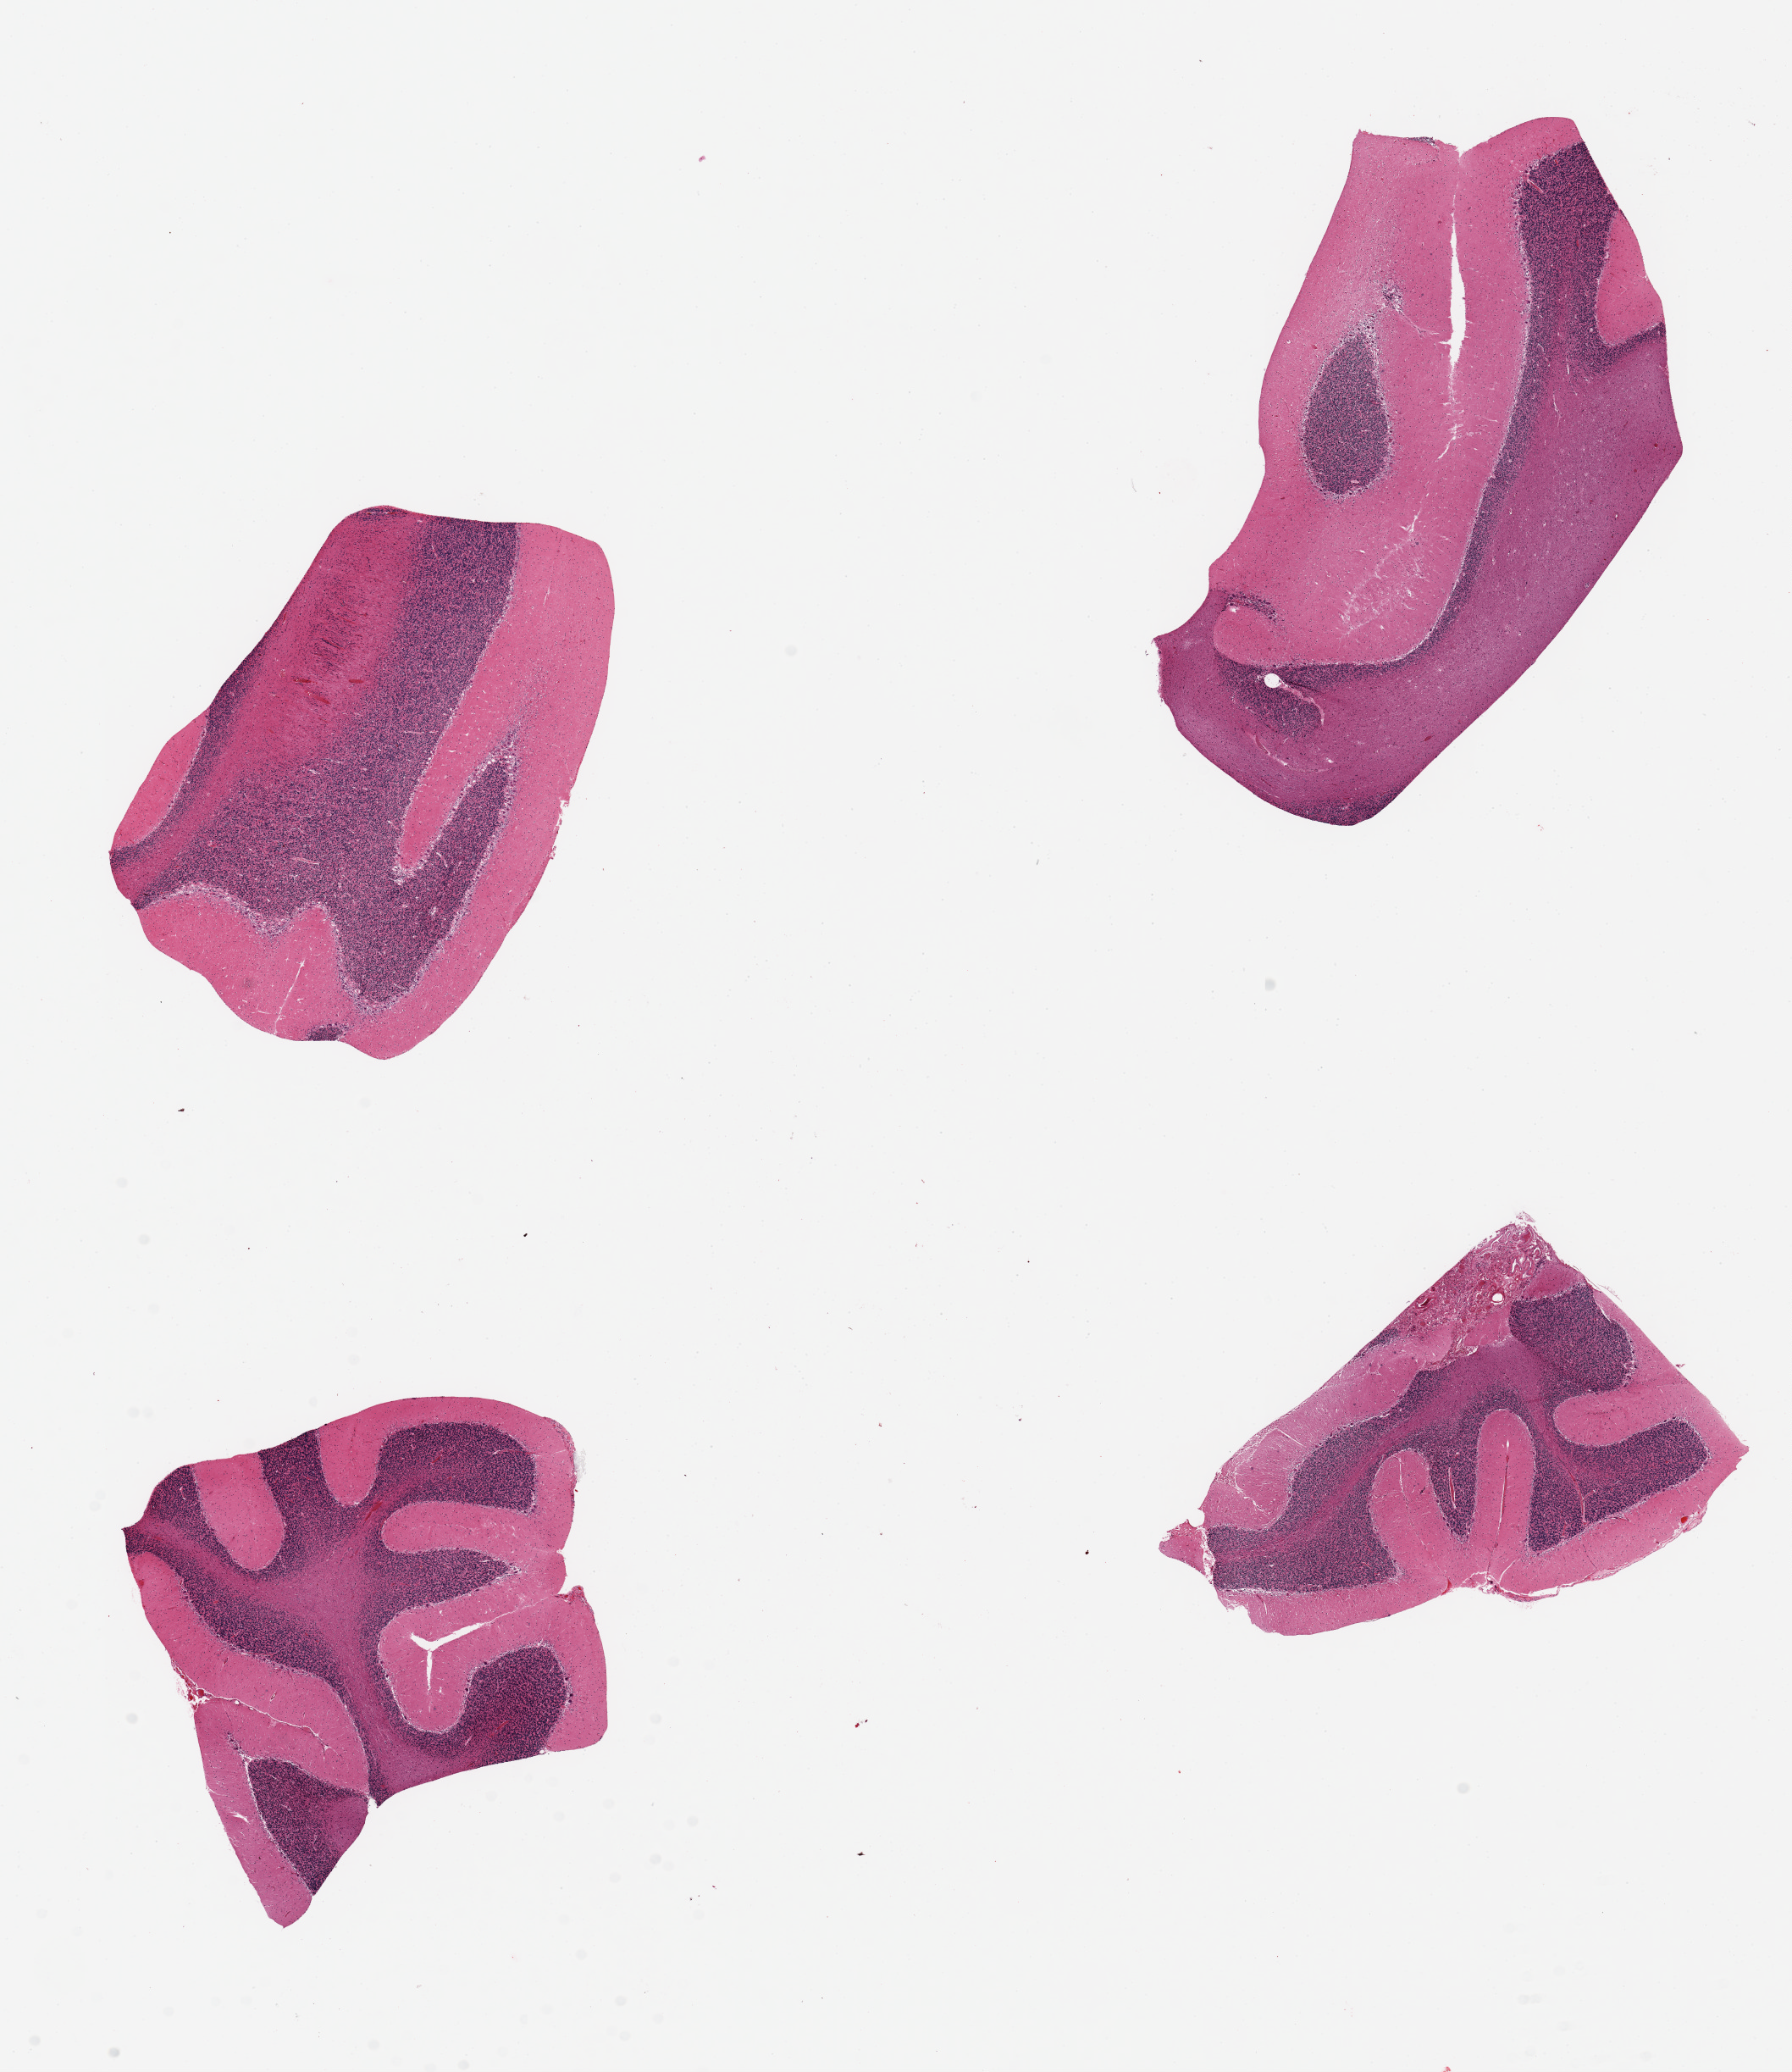
Whole-slide image, haematoxylin and eosin stain, a low-resolution overview of the entire scanned area, about 16.7 x 19.3 mm (slide scanned at 20x), PAXgene-fixed, paraffin-embedded tissue, sampled site (target tissue): cerebellum, donor tissue sample. Male donor.
- reviewer comment on this tissue sample: 4 pieces ~6x4mm. Purkinjes show minimal hypoxic damage